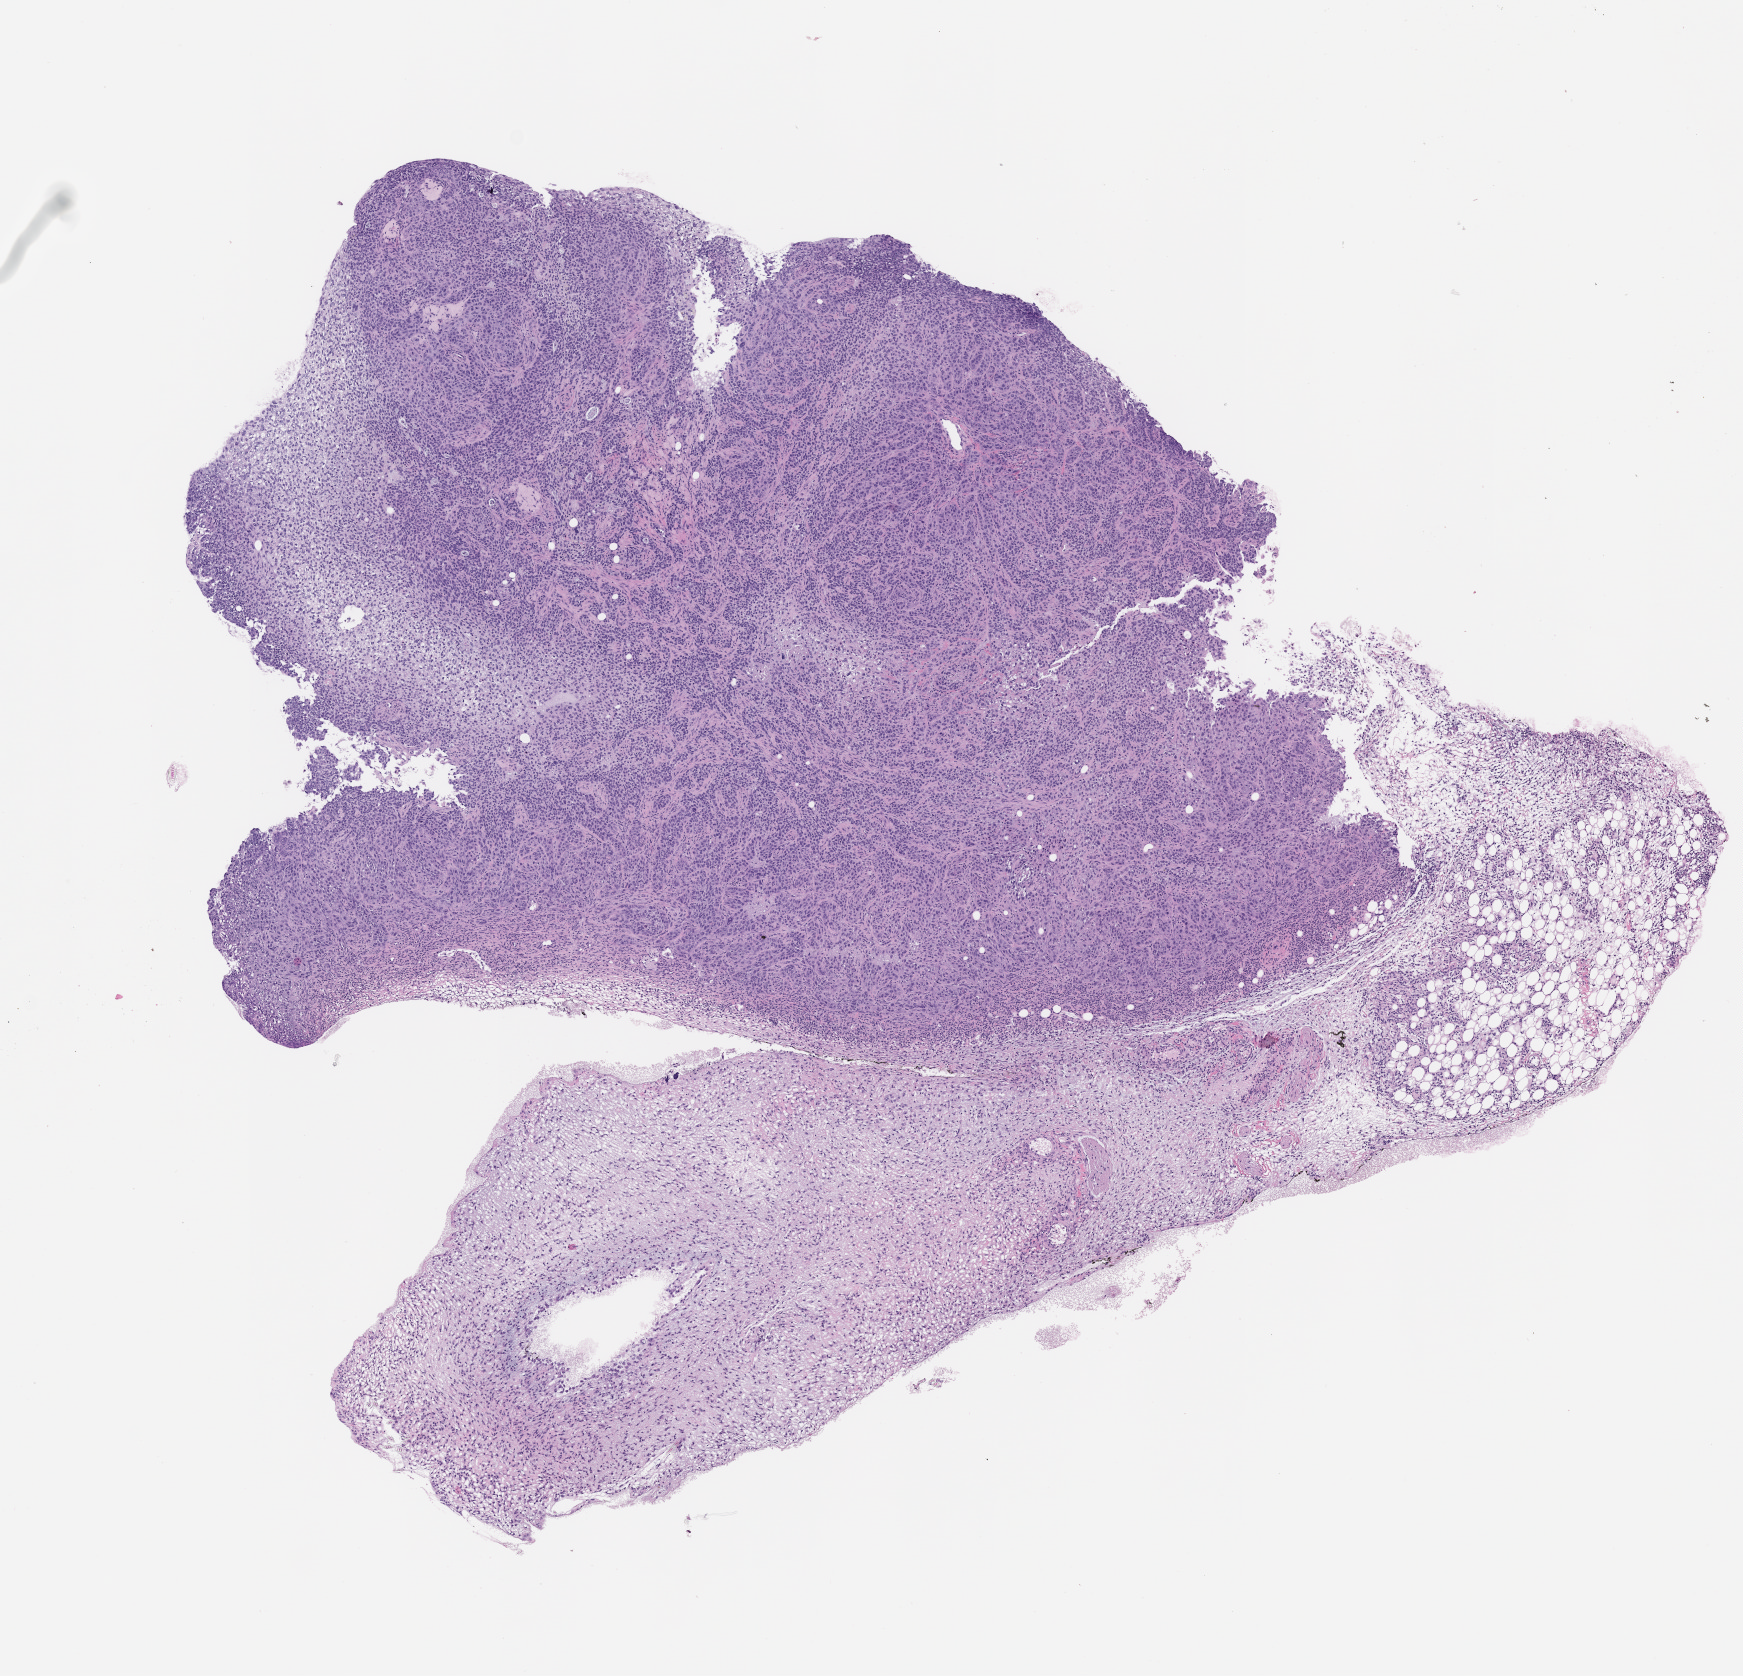
Whole-slide image, haematoxylin and eosin: patient-derived xenograft (human tumor grown in a mouse), passage 2 — low-resolution overview of the scanned area, about 7.0 x 6.7 mm, FFPE section, originating tumor site category: bladder.
Originating patient diagnosis: Transitional Cell Carcinoma.